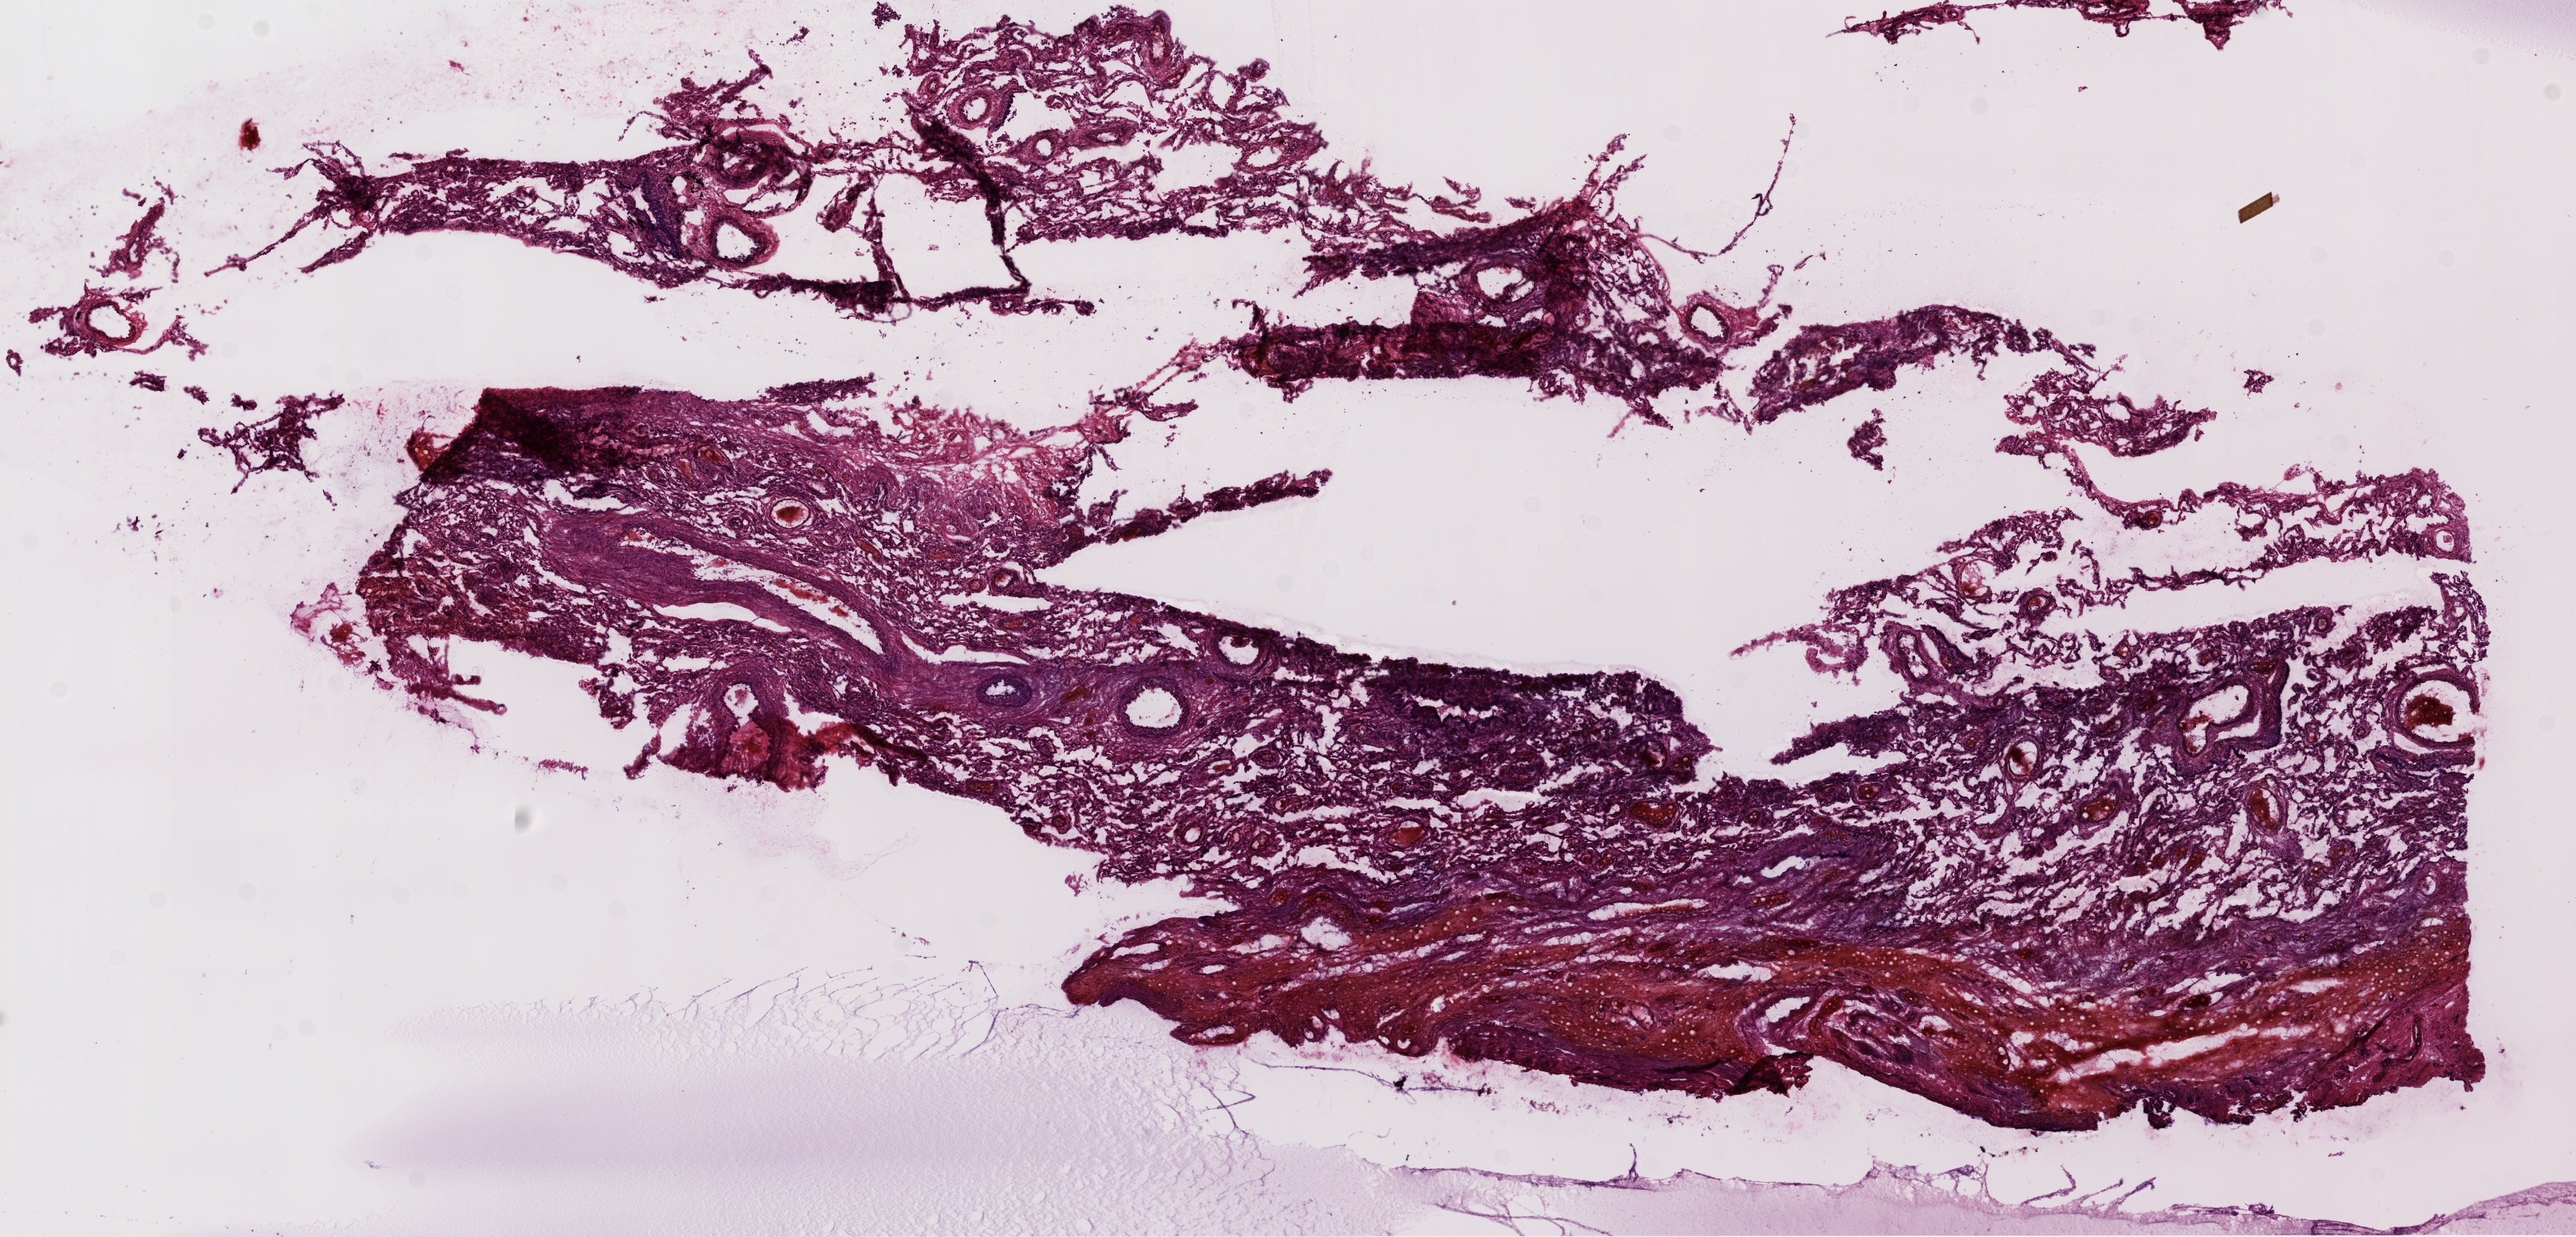
Whole-slide histology image, H&E-stained, low-resolution overview of the scanned area, about 15.0 x 7.2 mm (slide scanned at 20x), frozen section from the top of the tissue portion, lung, solid tissue normal (non-tumour tissue) sample. Male, age 70 years at initial diagnosis.
- this section: solid tissue normal (non-tumour) sample from the same patient
- patient diagnosis: Squamous cell carcinoma, NOS